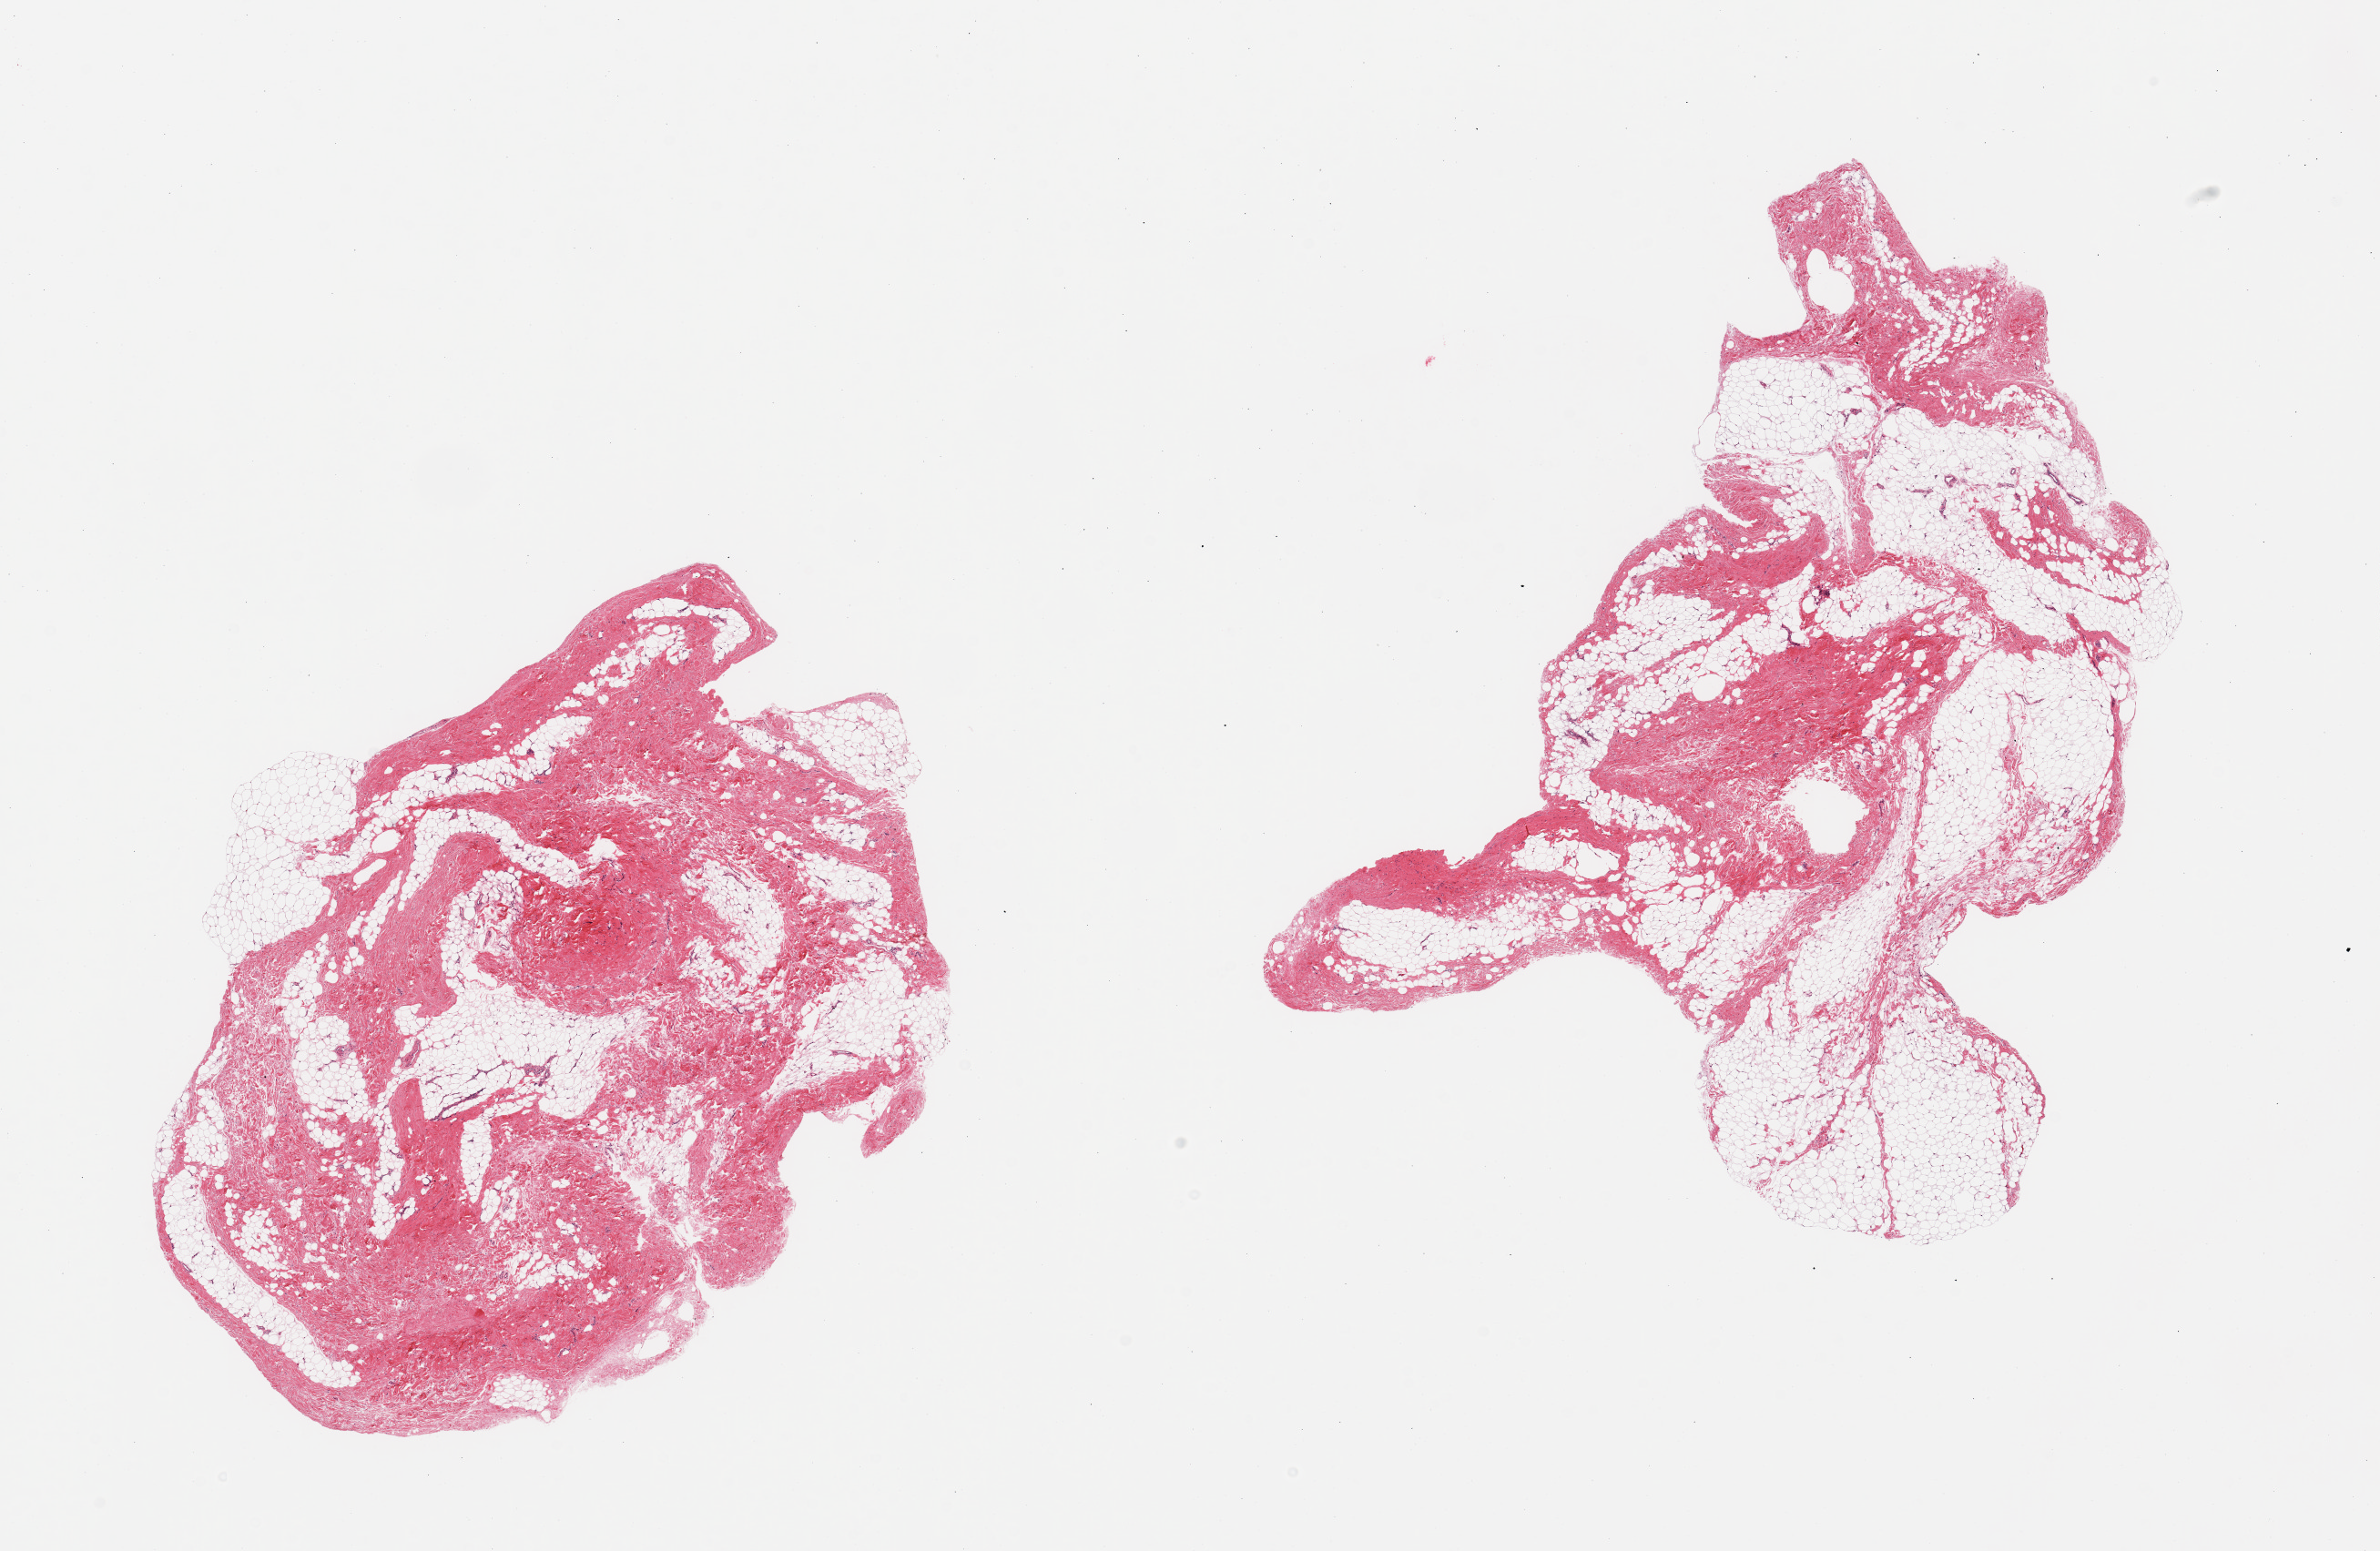
H&E whole-slide image, brightfield — a low-resolution overview of the entire scanned area, about 20.7 x 13.5 mm (from a 20x scan); PAXgene-fixed paraffin-embedded (PFPE) section; target tissue: breast; tissue donor sample. Male donor.
- reviewer comment on this tissue sample: 2 pieces; fibroadipose tissue without mammary tissue